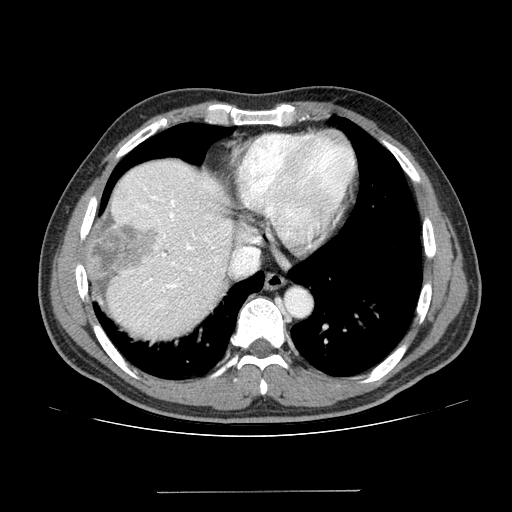
Contrast-enhanced abdominal CT (liver protocol), one axial slice; slice 116 of 131 in the series (ordered by position); reconstruction kernel STANDARD; one of 2 acquisitions stored at this slice position; soft-tissue window (W 400 / L 40 HU); 2.5 mm slice thickness; 512 × 512 image matrix, field of view 380 × 380 mm. From the clinical record (not read from this slice): diagnosis: hepatocellular carcinoma (patient treated with transarterial chemoembolisation; whether this scan precedes or follows treatment is not stated here); TNM stage (as recorded): Stage-I; Child-Pugh class: A; tumour differentiation: poorly differentiated; tumour nodularity: uninodular.
Outlined on this slice (semi-automatic segmentation, software-assisted and operator-edited):
- liver parenchyma outside the tumour (the mass and vessels are separate outlines, so this box may not span the whole liver): bounding box <86,158,234,338> (left, top, right, bottom; pixels)
- mass: <92,220,156,275>
- liver vessels: <113,165,227,323>